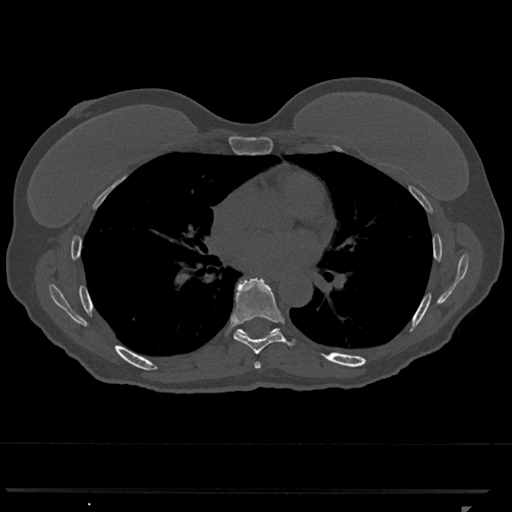
CT including the spine, one axial slice. Slice 705 of 793 in the series (ordered by position). Reconstruction kernel Br40s/3. Bone window (W 1800 / L 400 HU). 0.5 mm slice thickness. 512 × 512 image matrix, field of view 380 × 380 mm. Female patient, age 62 years. From the clinical record (not read from this slice): primary cancer: renal.
Structures marked on this image (semi-automatically segmented with operator editing):
- T6 vertebra: bounding box (x1, y1, x2, y2) in pixels: (254, 362, 261, 369)
- T7 vertebra: (231, 277, 295, 354)
- T8 vertebra: (240, 329, 276, 333)